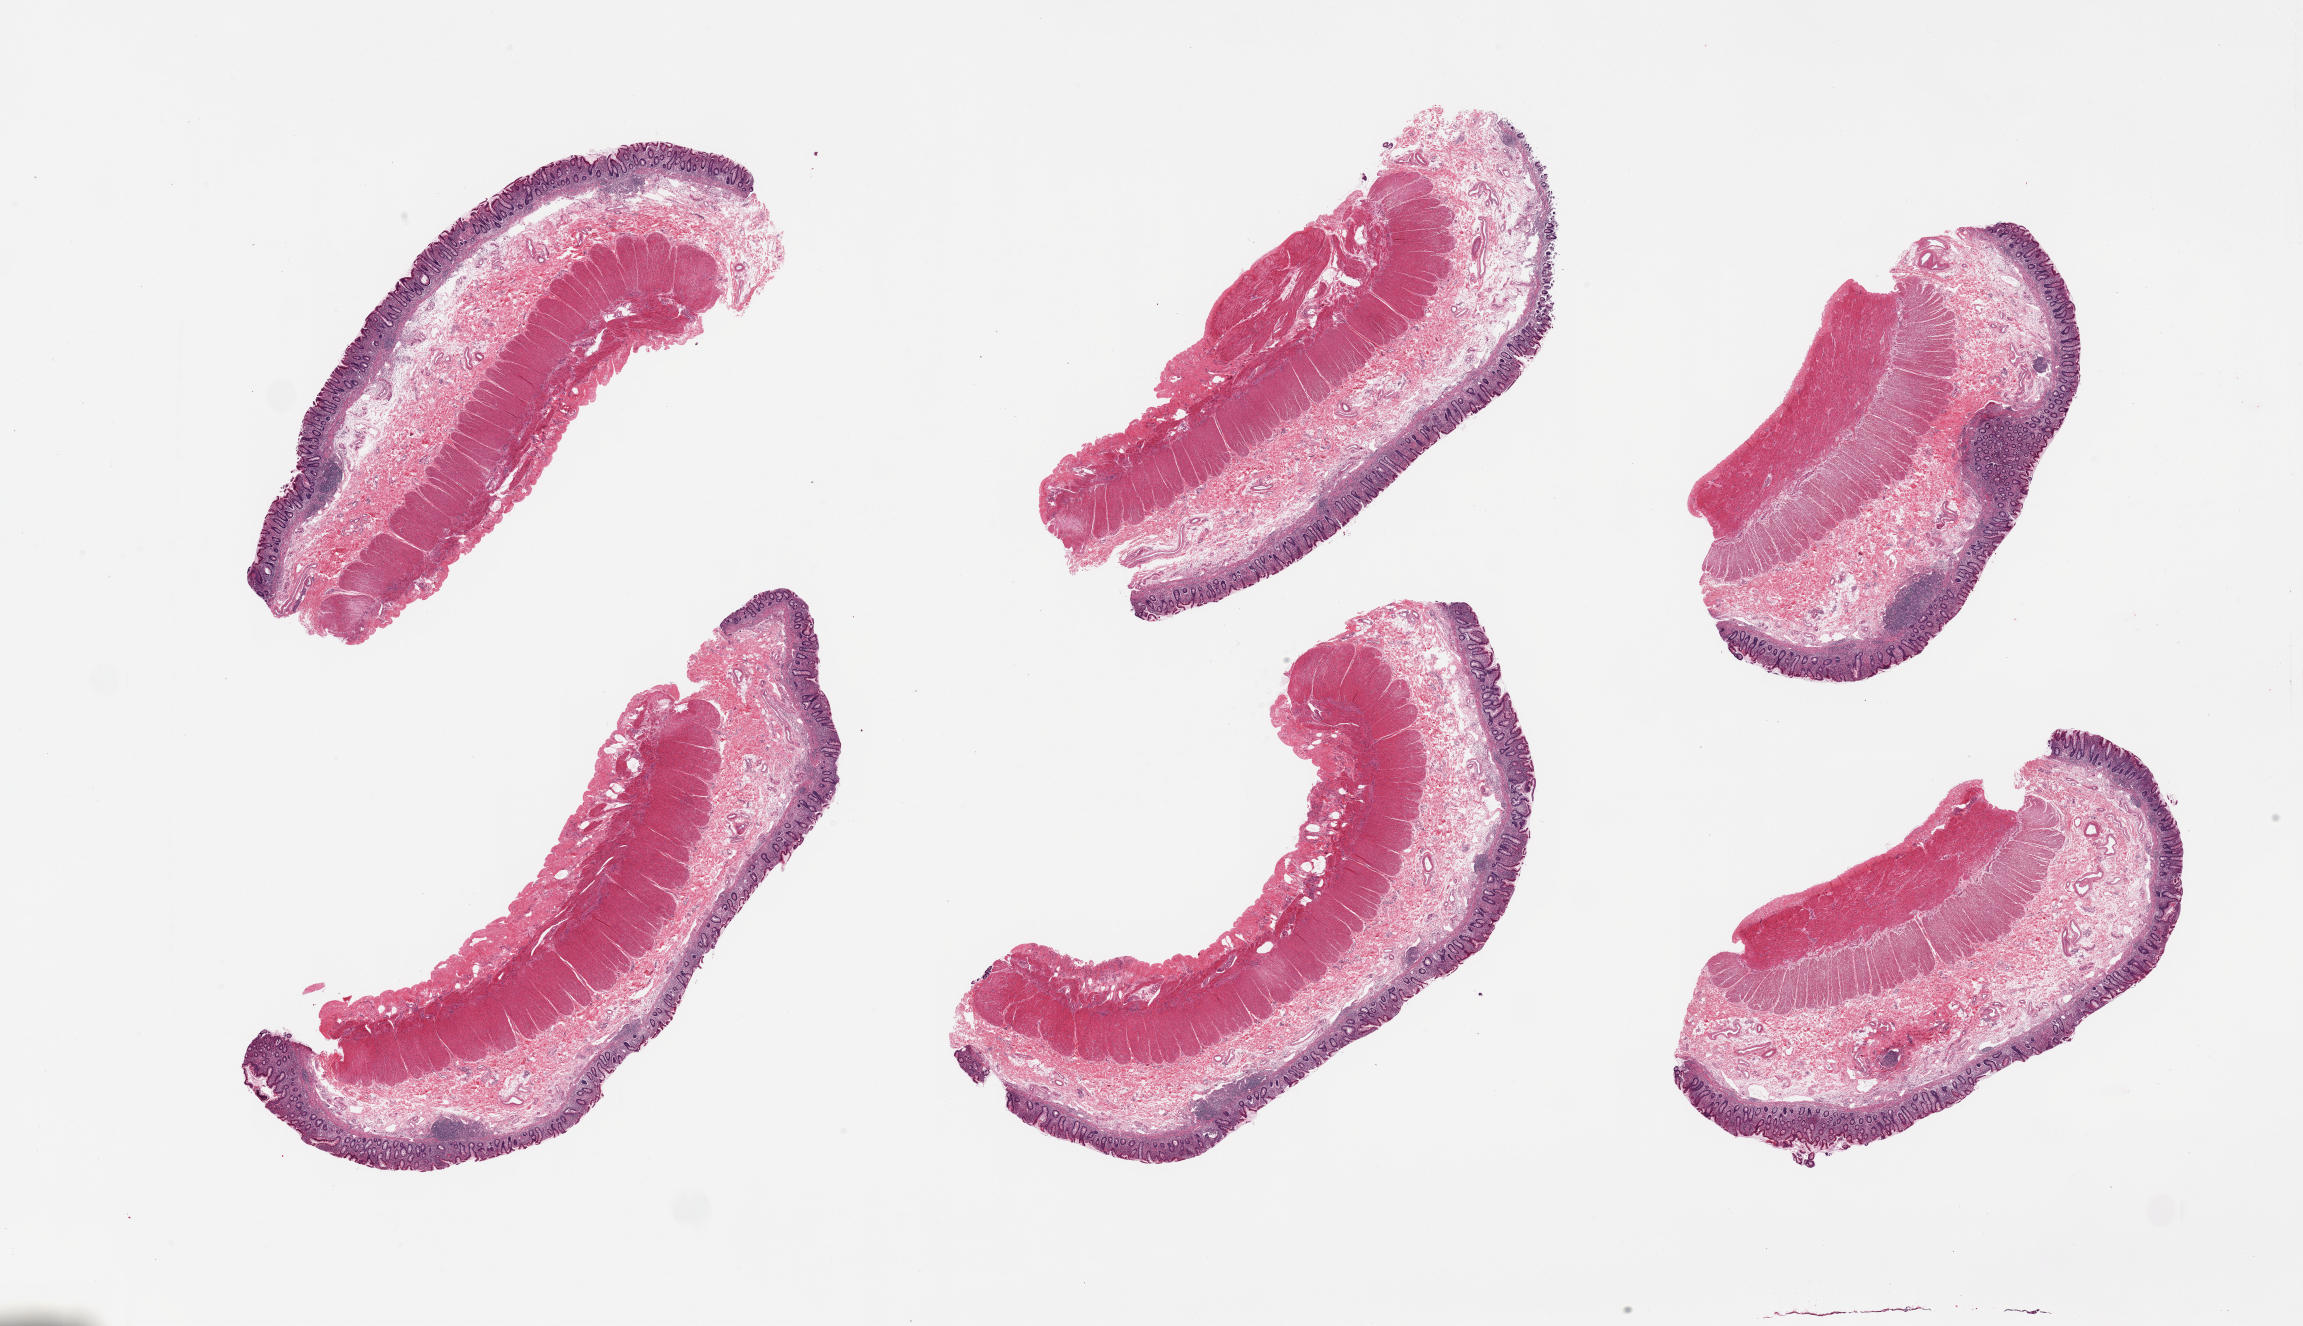
Digitized haematoxylin and eosin-stained section — shown as a low-resolution overview of the whole scanned area (about 36.4 x 21.0 mm), PAXgene-fixed paraffin-embedded (PFPE) section, sampled site (target tissue): transverse colon, donor tissue sample. Donor: female.
- reviewer comment on this tissue sample: 6 pieces, chronic inflammation with moderate architectural distortion c/w ulcerative colitis, no evidence of active disease